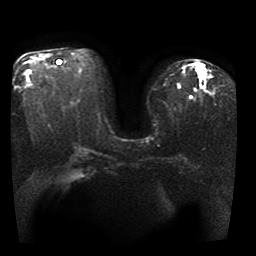
Breast MRI, one axial slice; slice 22 of 41 in the series (ordered by position); diffusion-weighted series; image 2 of 4 stored at this slice position (different b-values; order by instance number); 1.5 T; 5 mm slice thickness; 256 × 256 image matrix. Female patient.
Structures marked on this image (manually delineated by an expert):
- tumour on diffusion-weighted imaging: bounding box (x1, y1, x2, y2) in pixels: (196, 65, 201, 73)